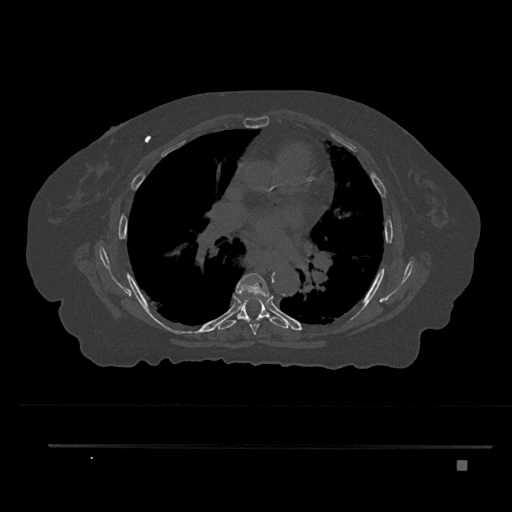
CT including the spine, one axial slice; slice 505 of 797 in the series (ordered by position); reconstruction kernel Br40s/3; 120 kVp; bone window (W 1800 / L 400 HU); 0.5 mm slice thickness; 512 × 512 image matrix, field of view 437 × 437 mm. Patient: female, 76 years. Case-level facts recorded for this patient, not image findings: primary cancer: lung; vertebrae with lytic lesions (as recorded): T11, L3.
Structures marked on this image (semi-automatically segmented with operator editing):
- T6 vertebra: box from (x=235, y=273) to (x=270, y=335) px
- T7 vertebra: (x=218, y=300)–(x=290, y=330)